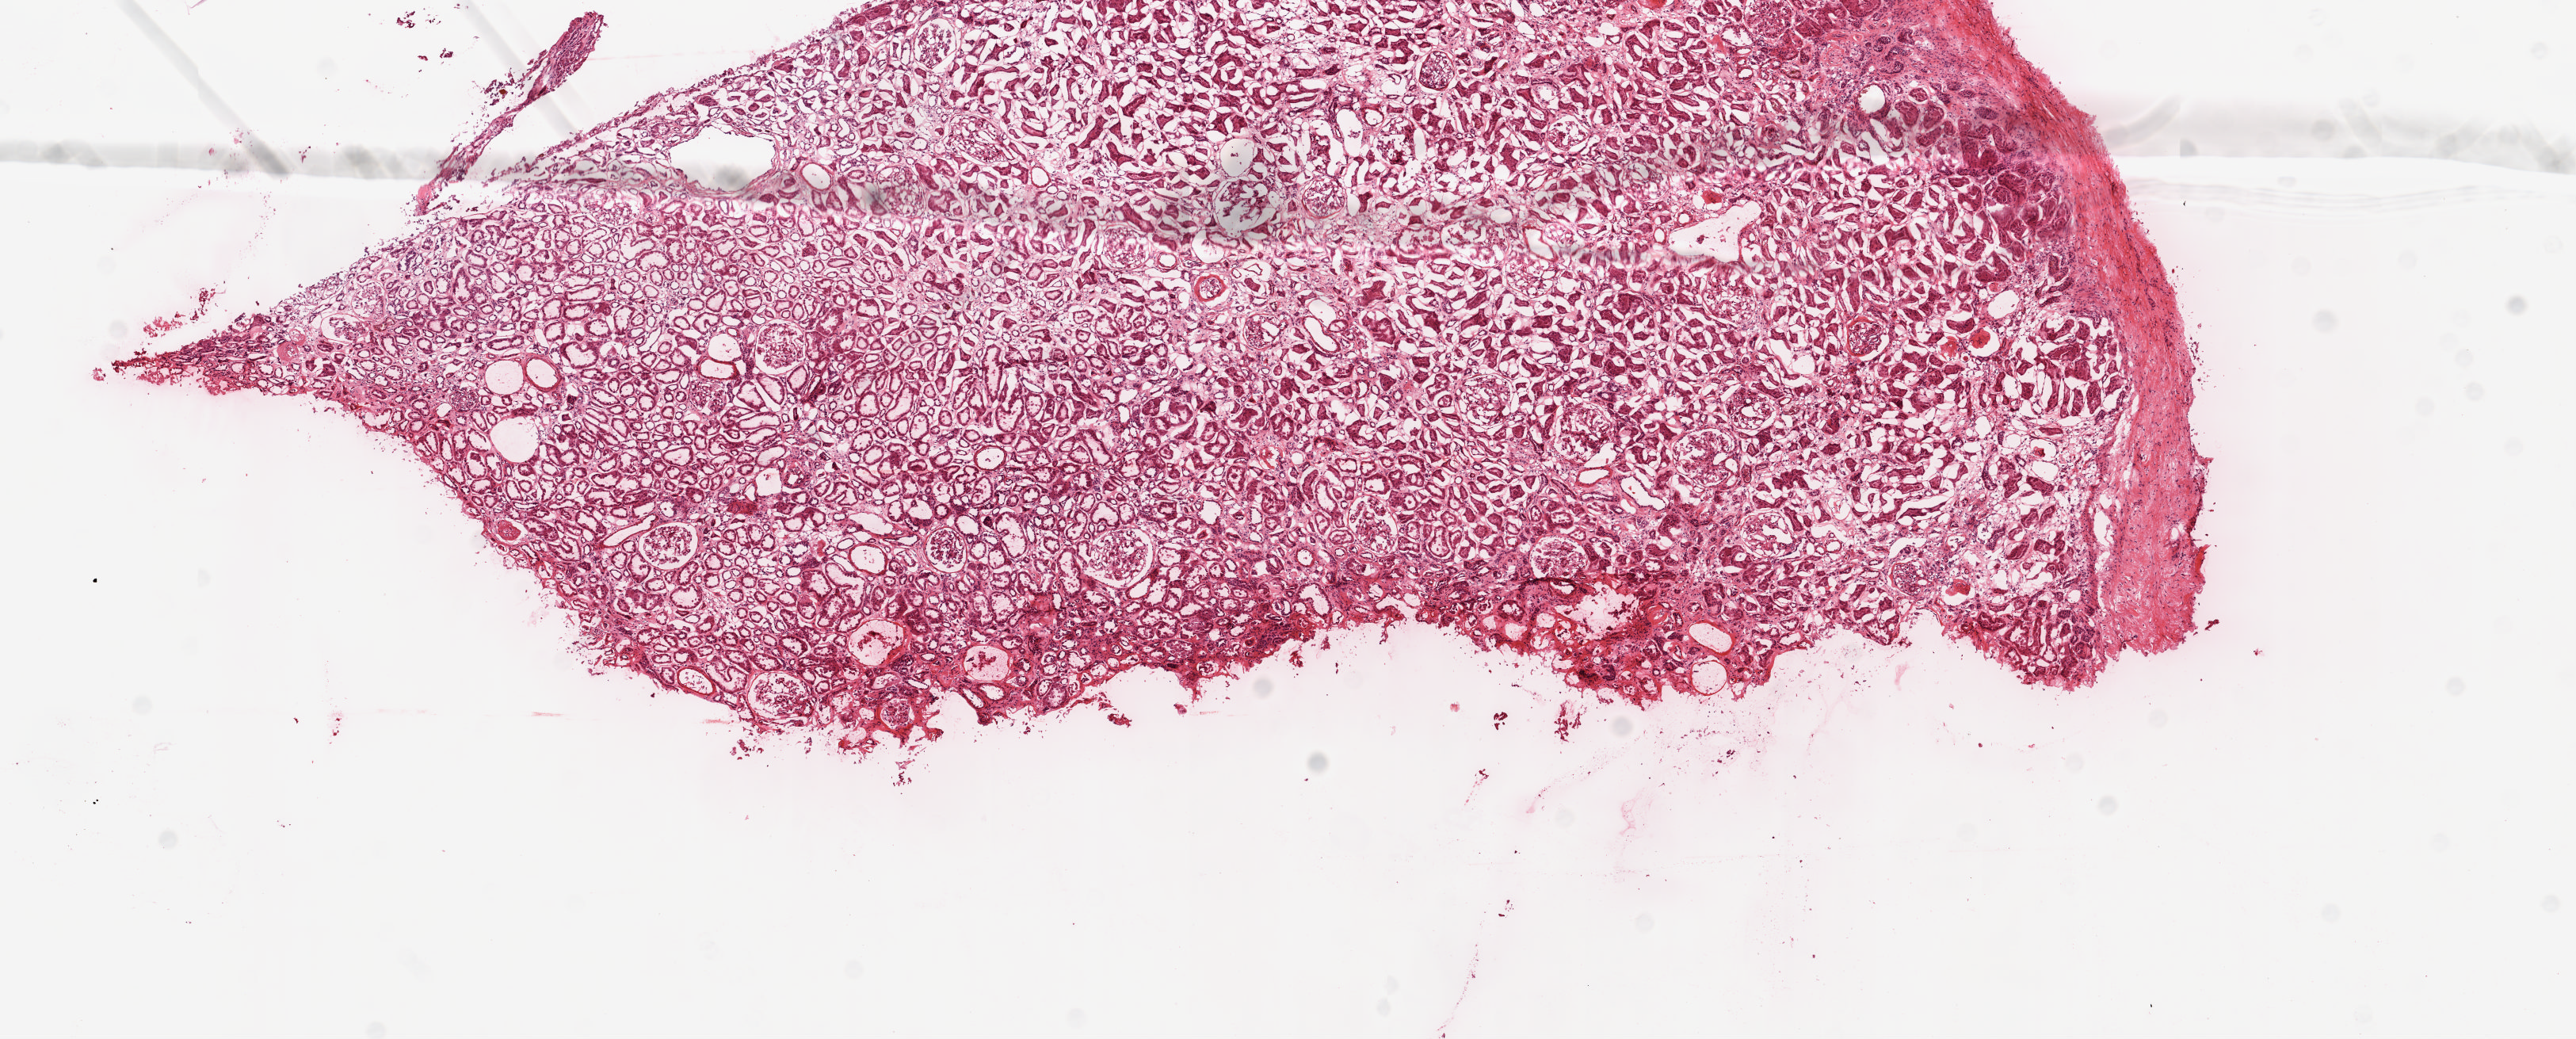
Digitized H&E tissue section (whole slide), a low-resolution overview of the entire scanned area, about 12.9 x 5.2 mm; frozen section; sample: solid tissue normal (non-tumour tissue), kidney. Female patient; age at initial diagnosis 76 years.
This section: solid tissue normal sample (biorepository sample class). Patient diagnosis: Clear cell adenocarcinoma, NOS.